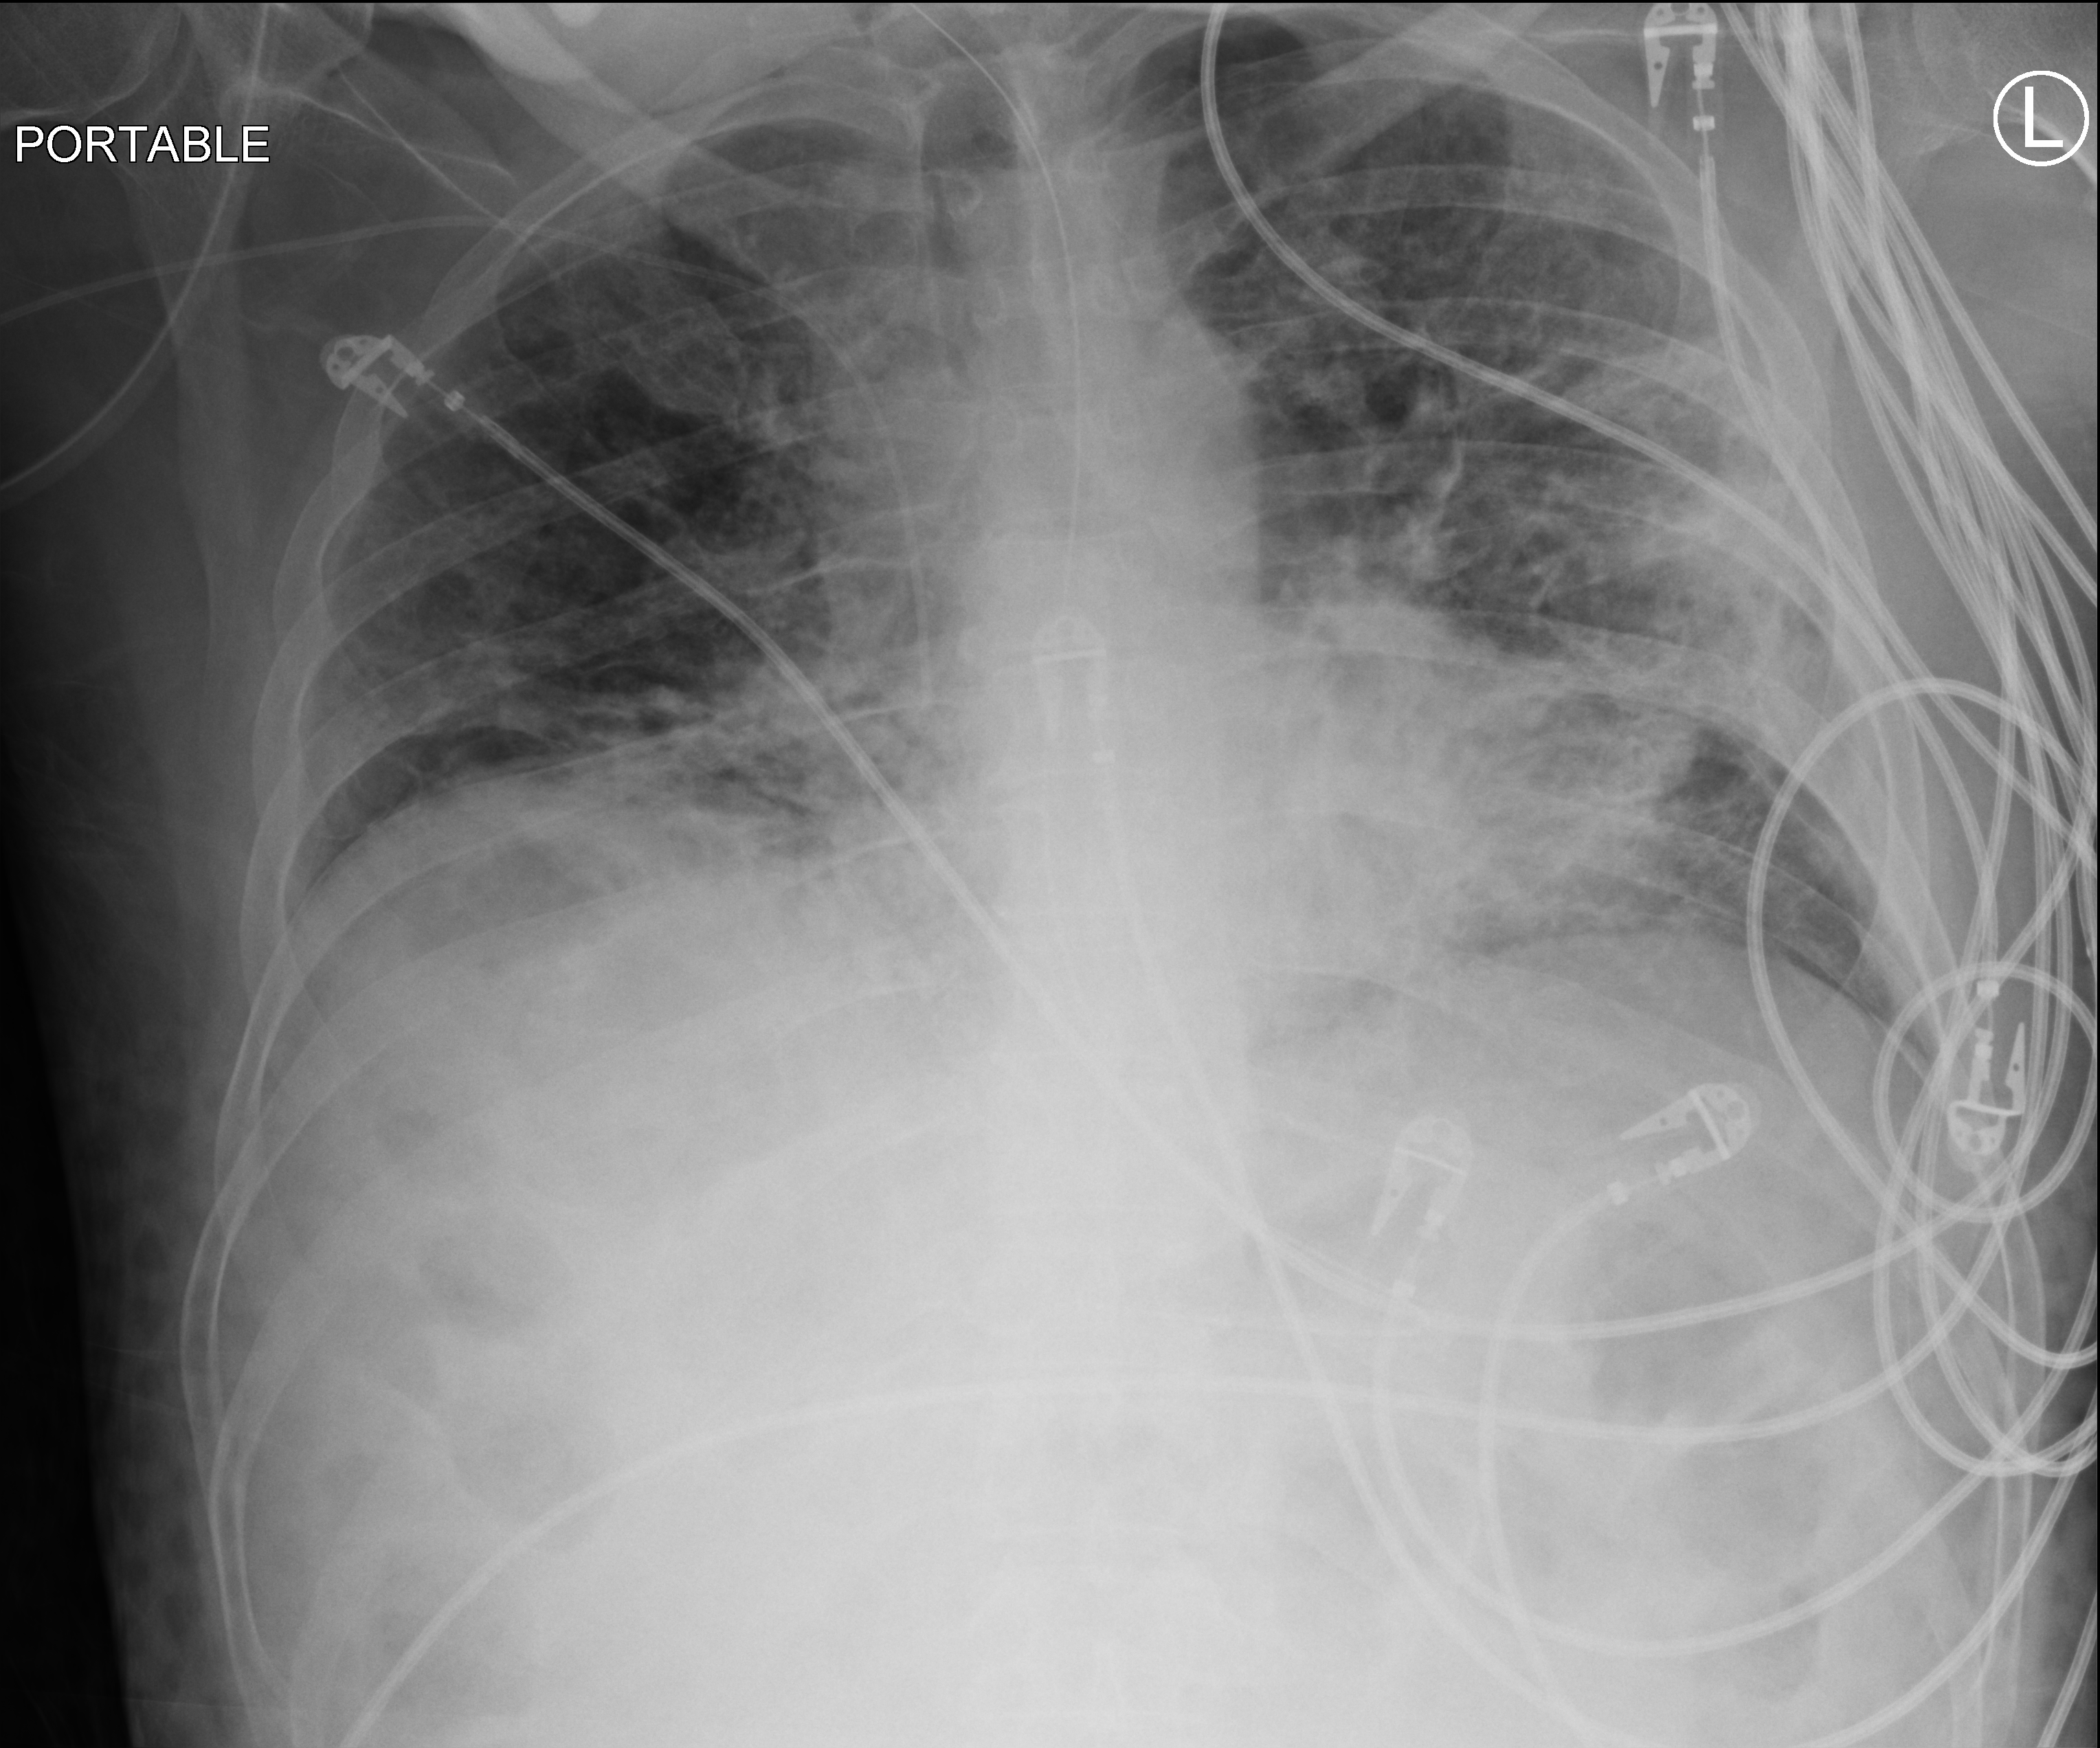
Portable chest radiograph, anteroposterior (AP) projection. Patient hospitalised with COVID-19; male, aged 18–59 years.
Hospital-stay facts (about this admission, not read from this image; timing relative to this image not recorded): mechanically ventilated during this hospital stay: yes; COPD (admission record): no; admitted to intensive care during this hospital stay: yes.